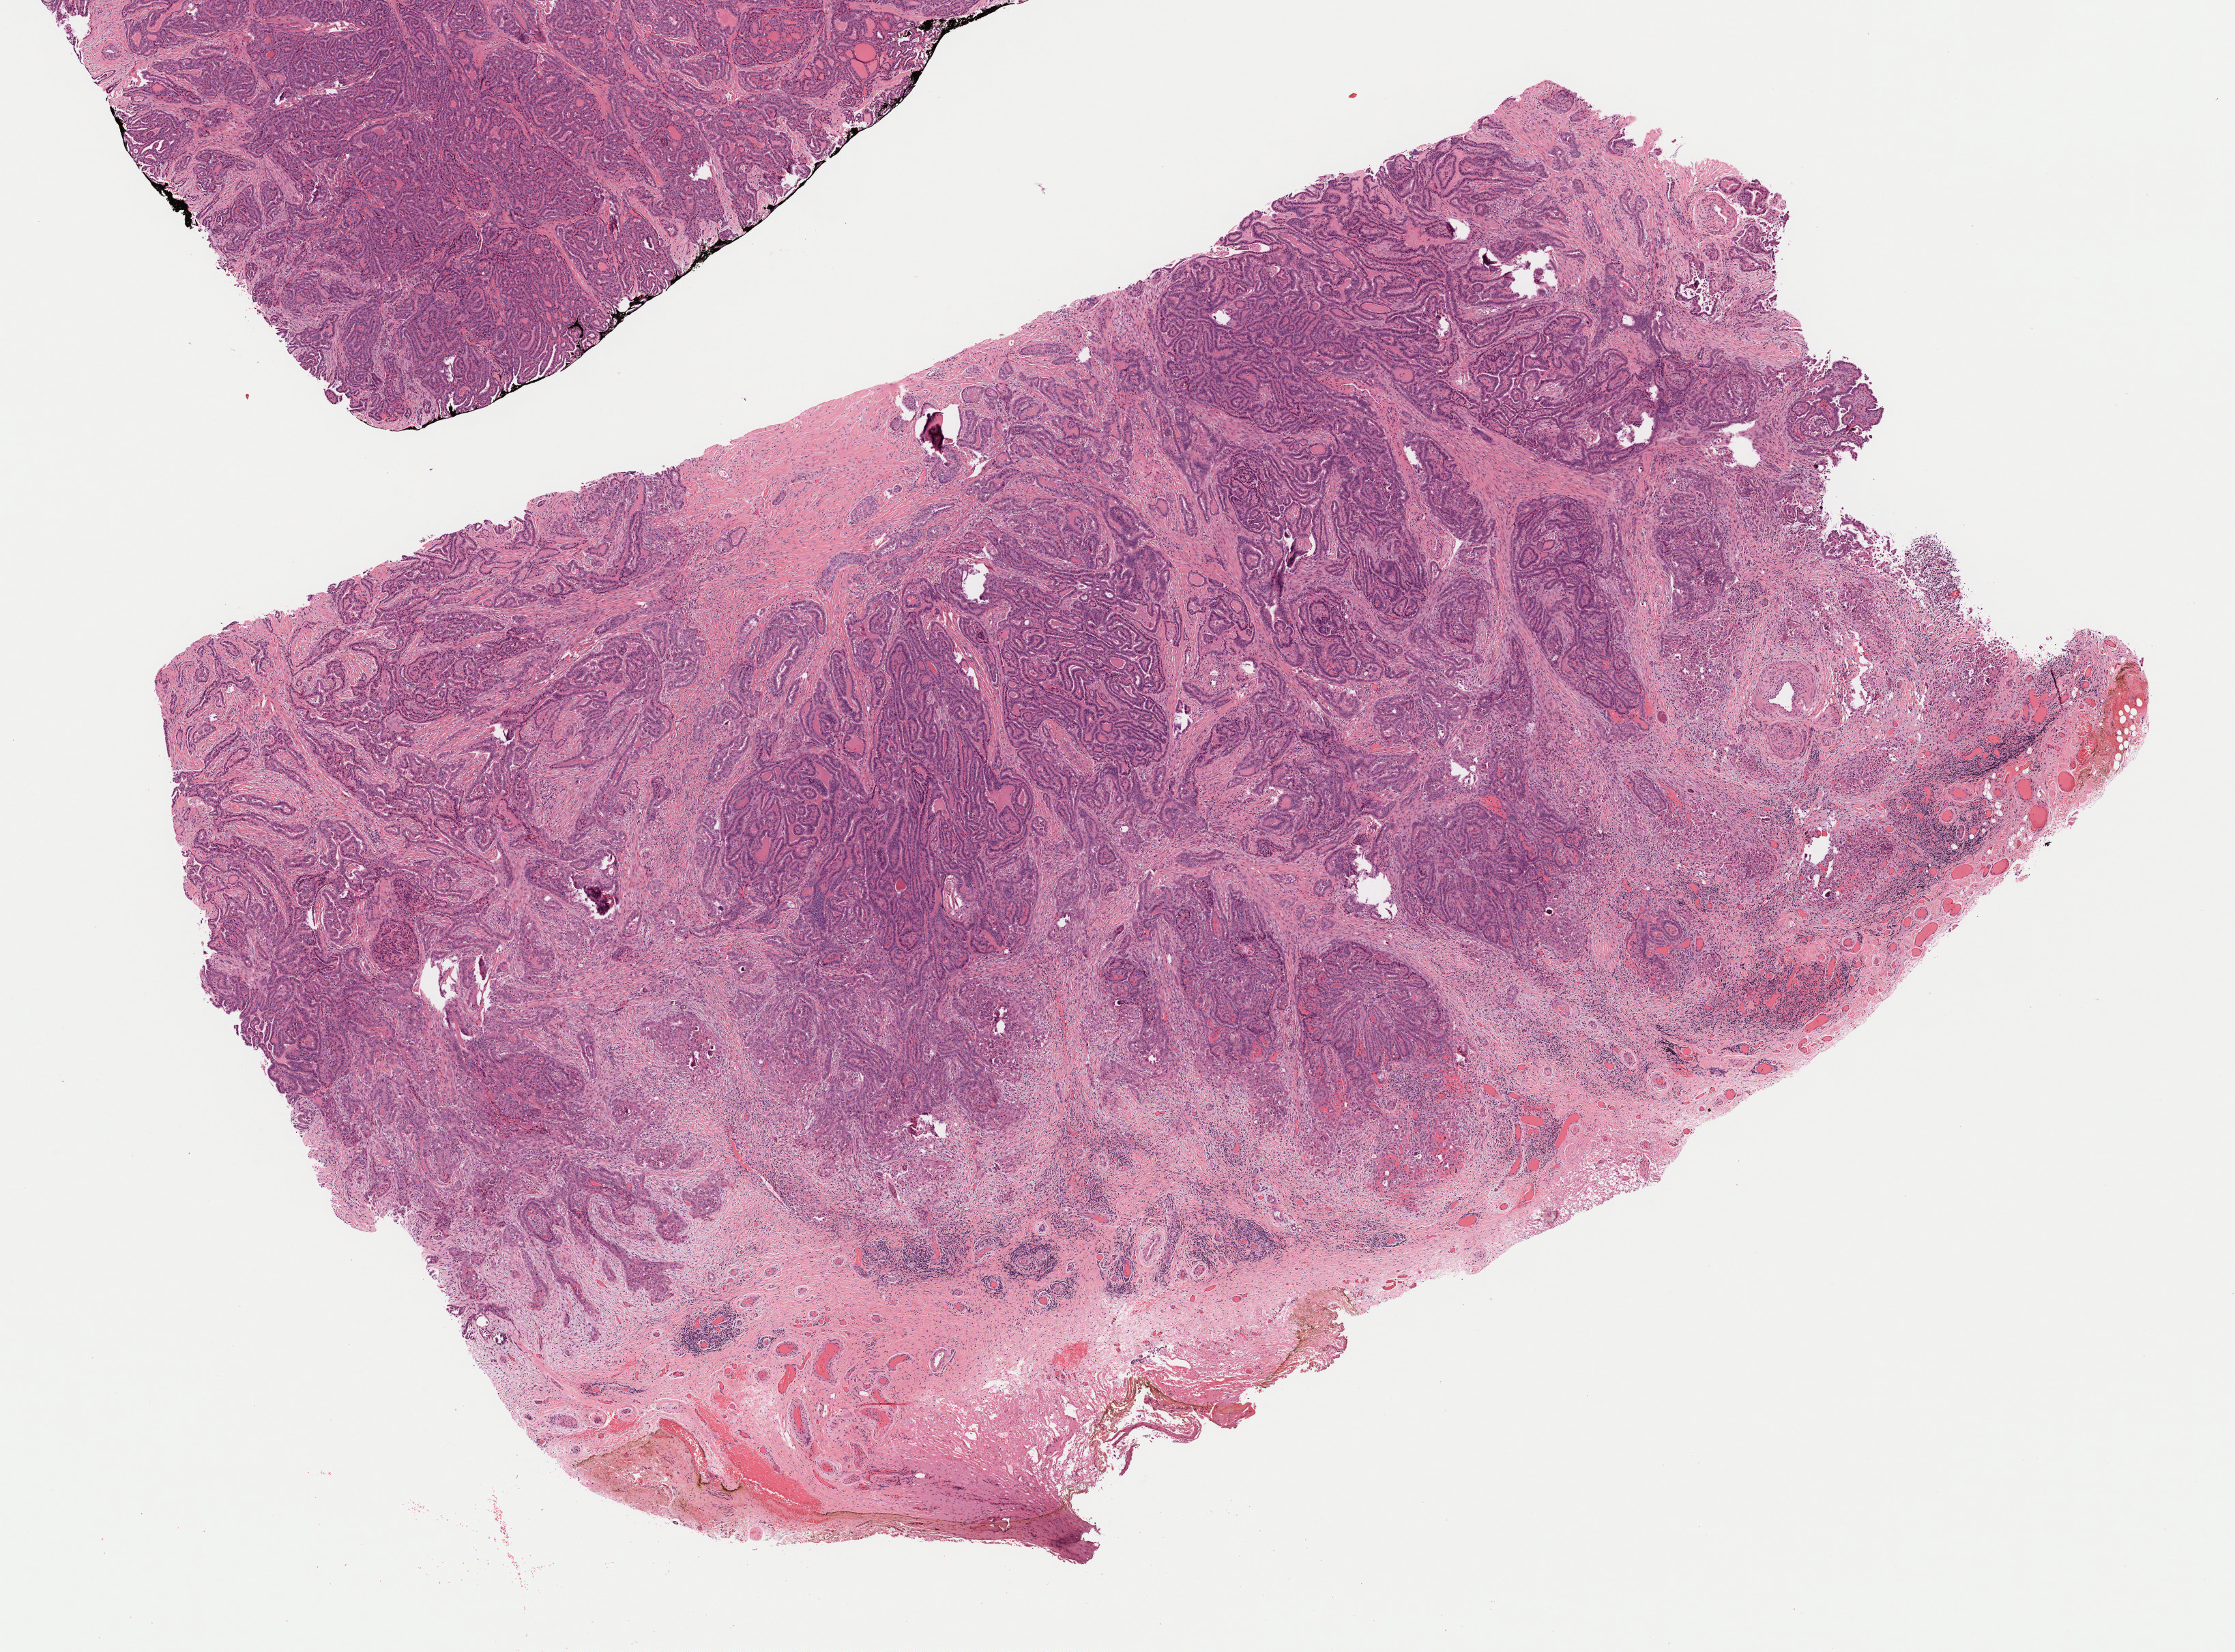
Digitized H&E-stained tissue section (whole slide) — a low-resolution overview of the entire scanned area, about 13.2 x 9.8 mm (from a 40x scan). FFPE section. Primary tumour sample from the thyroid. Female, age 59 years at initial diagnosis.
- AJCC pathologic stage: IVA (7th edition)
- diagnosis: Papillary adenocarcinoma, NOS
- lymph nodes positive (case pathology): 12 of 40 examined